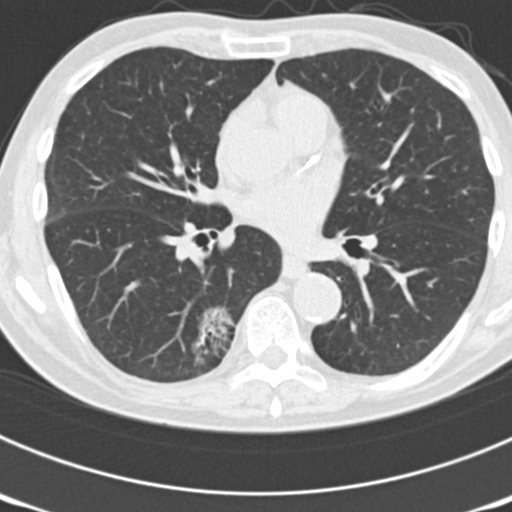
Low-dose screening chest CT, axial slice. Third screening round (two years after baseline). Lung window (W 1500 / L -600 HU). Standard (soft-tissue) reconstruction kernel (B30f). Male participant, aged 70 years at enrolment. Current smoker at enrolment.
• Expert reader's lesion annotation, box from (x=148, y=302) to (x=238, y=385) px.
• The screening reader recorded 3 non-calcified nodules or masses ≥4 mm on this exam (right upper lobe, left upper lobe, right lower lobe); which of them this box marks is not recorded.
• Participant outcome: lung cancer diagnosed 14 days after this screen — bronchiolo-alveolar adenocarcinoma, NOS, right lower lobe, poorly differentiated (G3), stage IB (AJCC 6th edition), 30 mm at pathology.